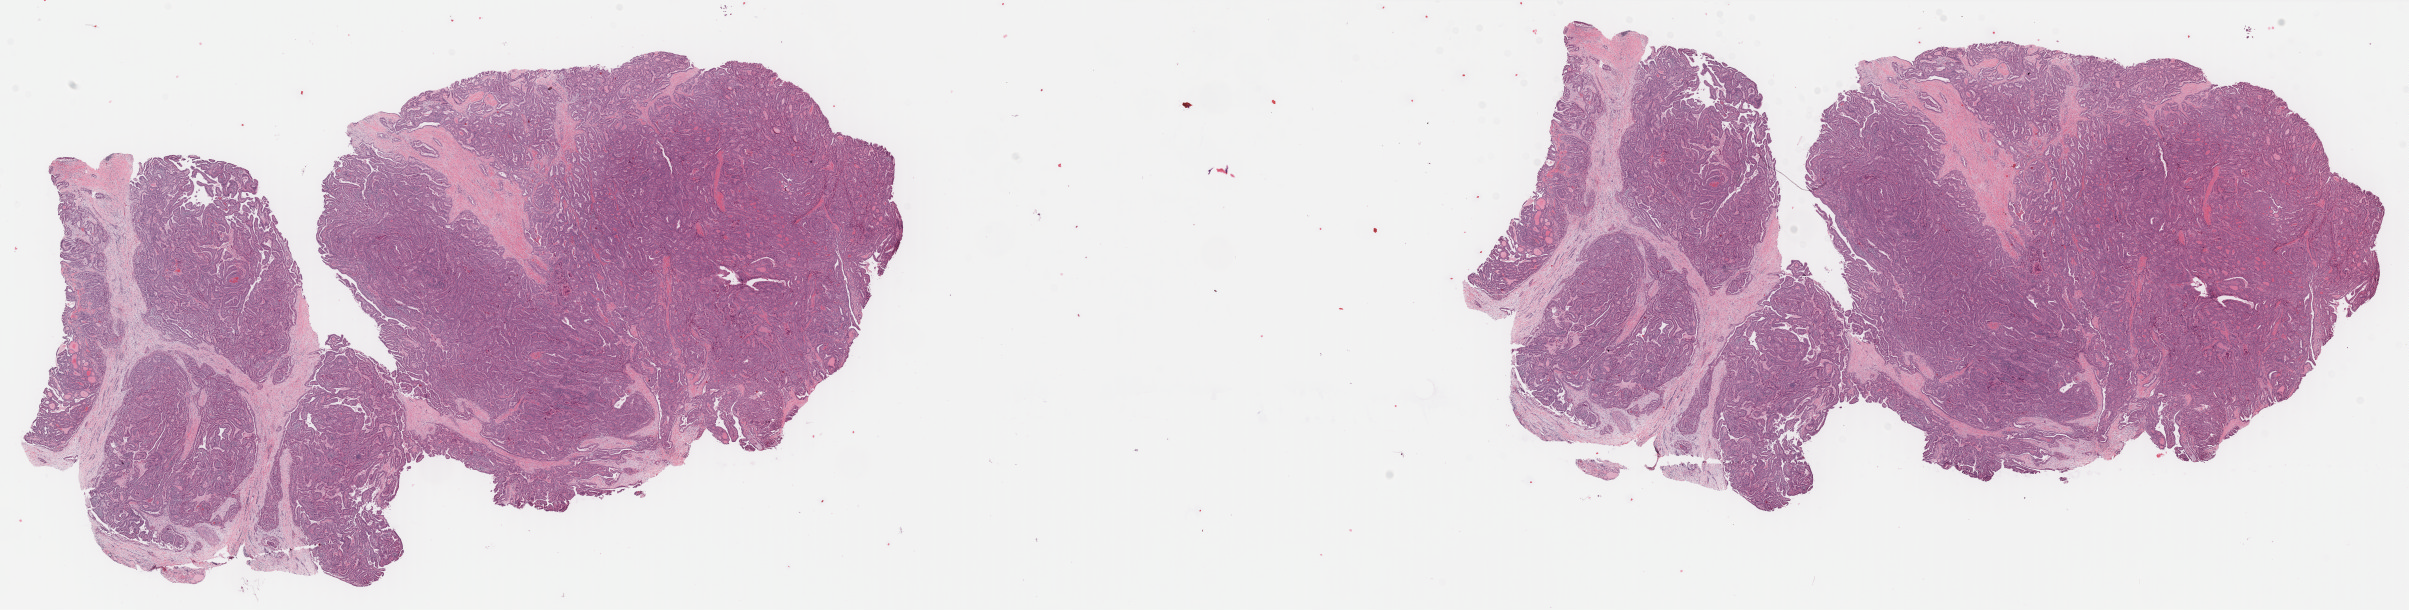
Whole-slide histology image, H&E, low-resolution overview of the scanned area, about 38.1 x 9.7 mm (from a 40x scan); formalin-fixed paraffin-embedded (FFPE) diagnostic section; sample: primary tumour, thyroid. Female patient; age at initial diagnosis 43 years.
Pathologic diagnosis: Papillary adenocarcinoma, NOS (thyroid gland). AJCC pathologic stage: I. Lymph nodes positive (case pathology): 1 of 1 examined. Laterality: right.